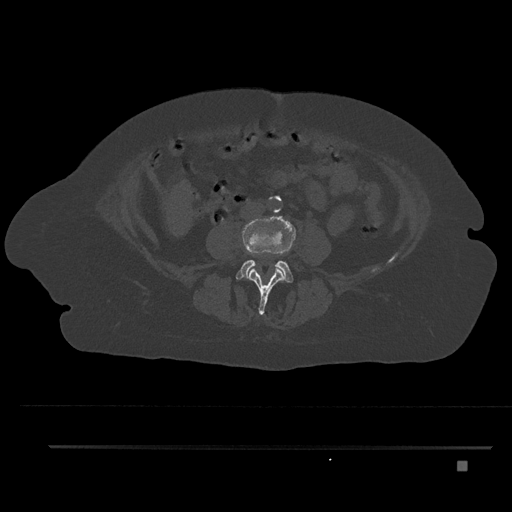
CT including the spine, one axial slice; slice 101 of 797 in the series (ordered by position); bone window (W 1800 / L 400 HU); 0.5 mm slice thickness; 512 × 512 image matrix. Patient: female, 76 years. Case-level facts recorded for this patient, not image findings: primary cancer: lung; vertebrae with lytic lesions (as recorded): T11, L3.
Annotated regions visible in this slice (semi-automatic segmentation, software-assisted and operator-edited):
- L3 vertebra: box from (x=249, y=219) to (x=285, y=315) px
- L4 vertebra: (x=235, y=216)–(x=296, y=283)